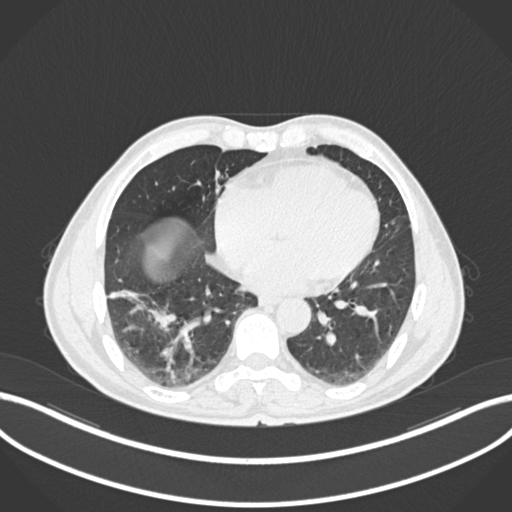
Chest CT, one axial slice. Slice 58 of 208 in the series (ordered by position). Reconstruction kernel B30f. Lung window (W 1500 / L -600 HU). 1 mm slice thickness. 512 × 512 image matrix. Patient: male, 58 years. Case-level facts recorded for this patient, not image findings: clinical TNM (as recorded): T3 N0 M0.
Outlined on this slice (rectangle marked by the reading radiologist):
- lung tumour (recorded histology: squamous cell carcinoma): bounding box (x1, y1, x2, y2) in pixels: (106, 278, 178, 333)